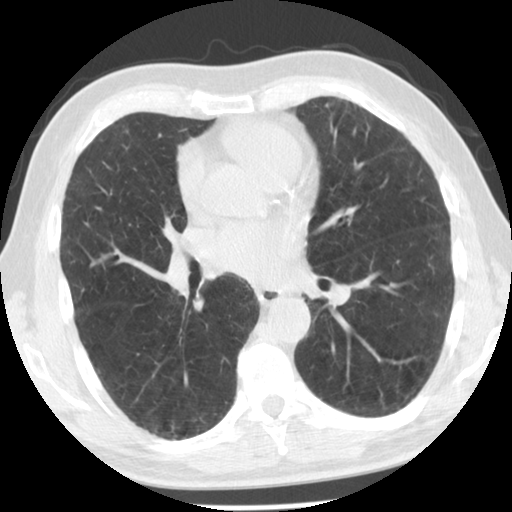
Axial slice from a low-dose chest CT screening exam; second annual screen; lung window (W 1500 / L -600 HU); 2.5 mm slice thickness; standard (soft-tissue) reconstruction kernel (STANDARD); 140 kVp; slice 65 of 129 in the series. Male participant, aged 66 years at enrolment. Former smoker at enrolment.
• Expert-annotated lung lesion, bounding box <308,89,346,125> (left, top, right, bottom; pixels).
• Screening reader's record for this exam (one nodule recorded; not confirmed to be the boxed lesion): non-calcified nodule or mass ≥4 mm, lingula, 6 × 5 mm, smooth margins, soft tissue attenuation, pre-existing on the prior screen: yes; interval growth: yes.
• Participant outcome: lung cancer diagnosed 148 days after this screen — adenocarcinoma, NOS, left upper lobe, moderately differentiated (G2), stage IIB (AJCC 6th edition), 9 mm at pathology.